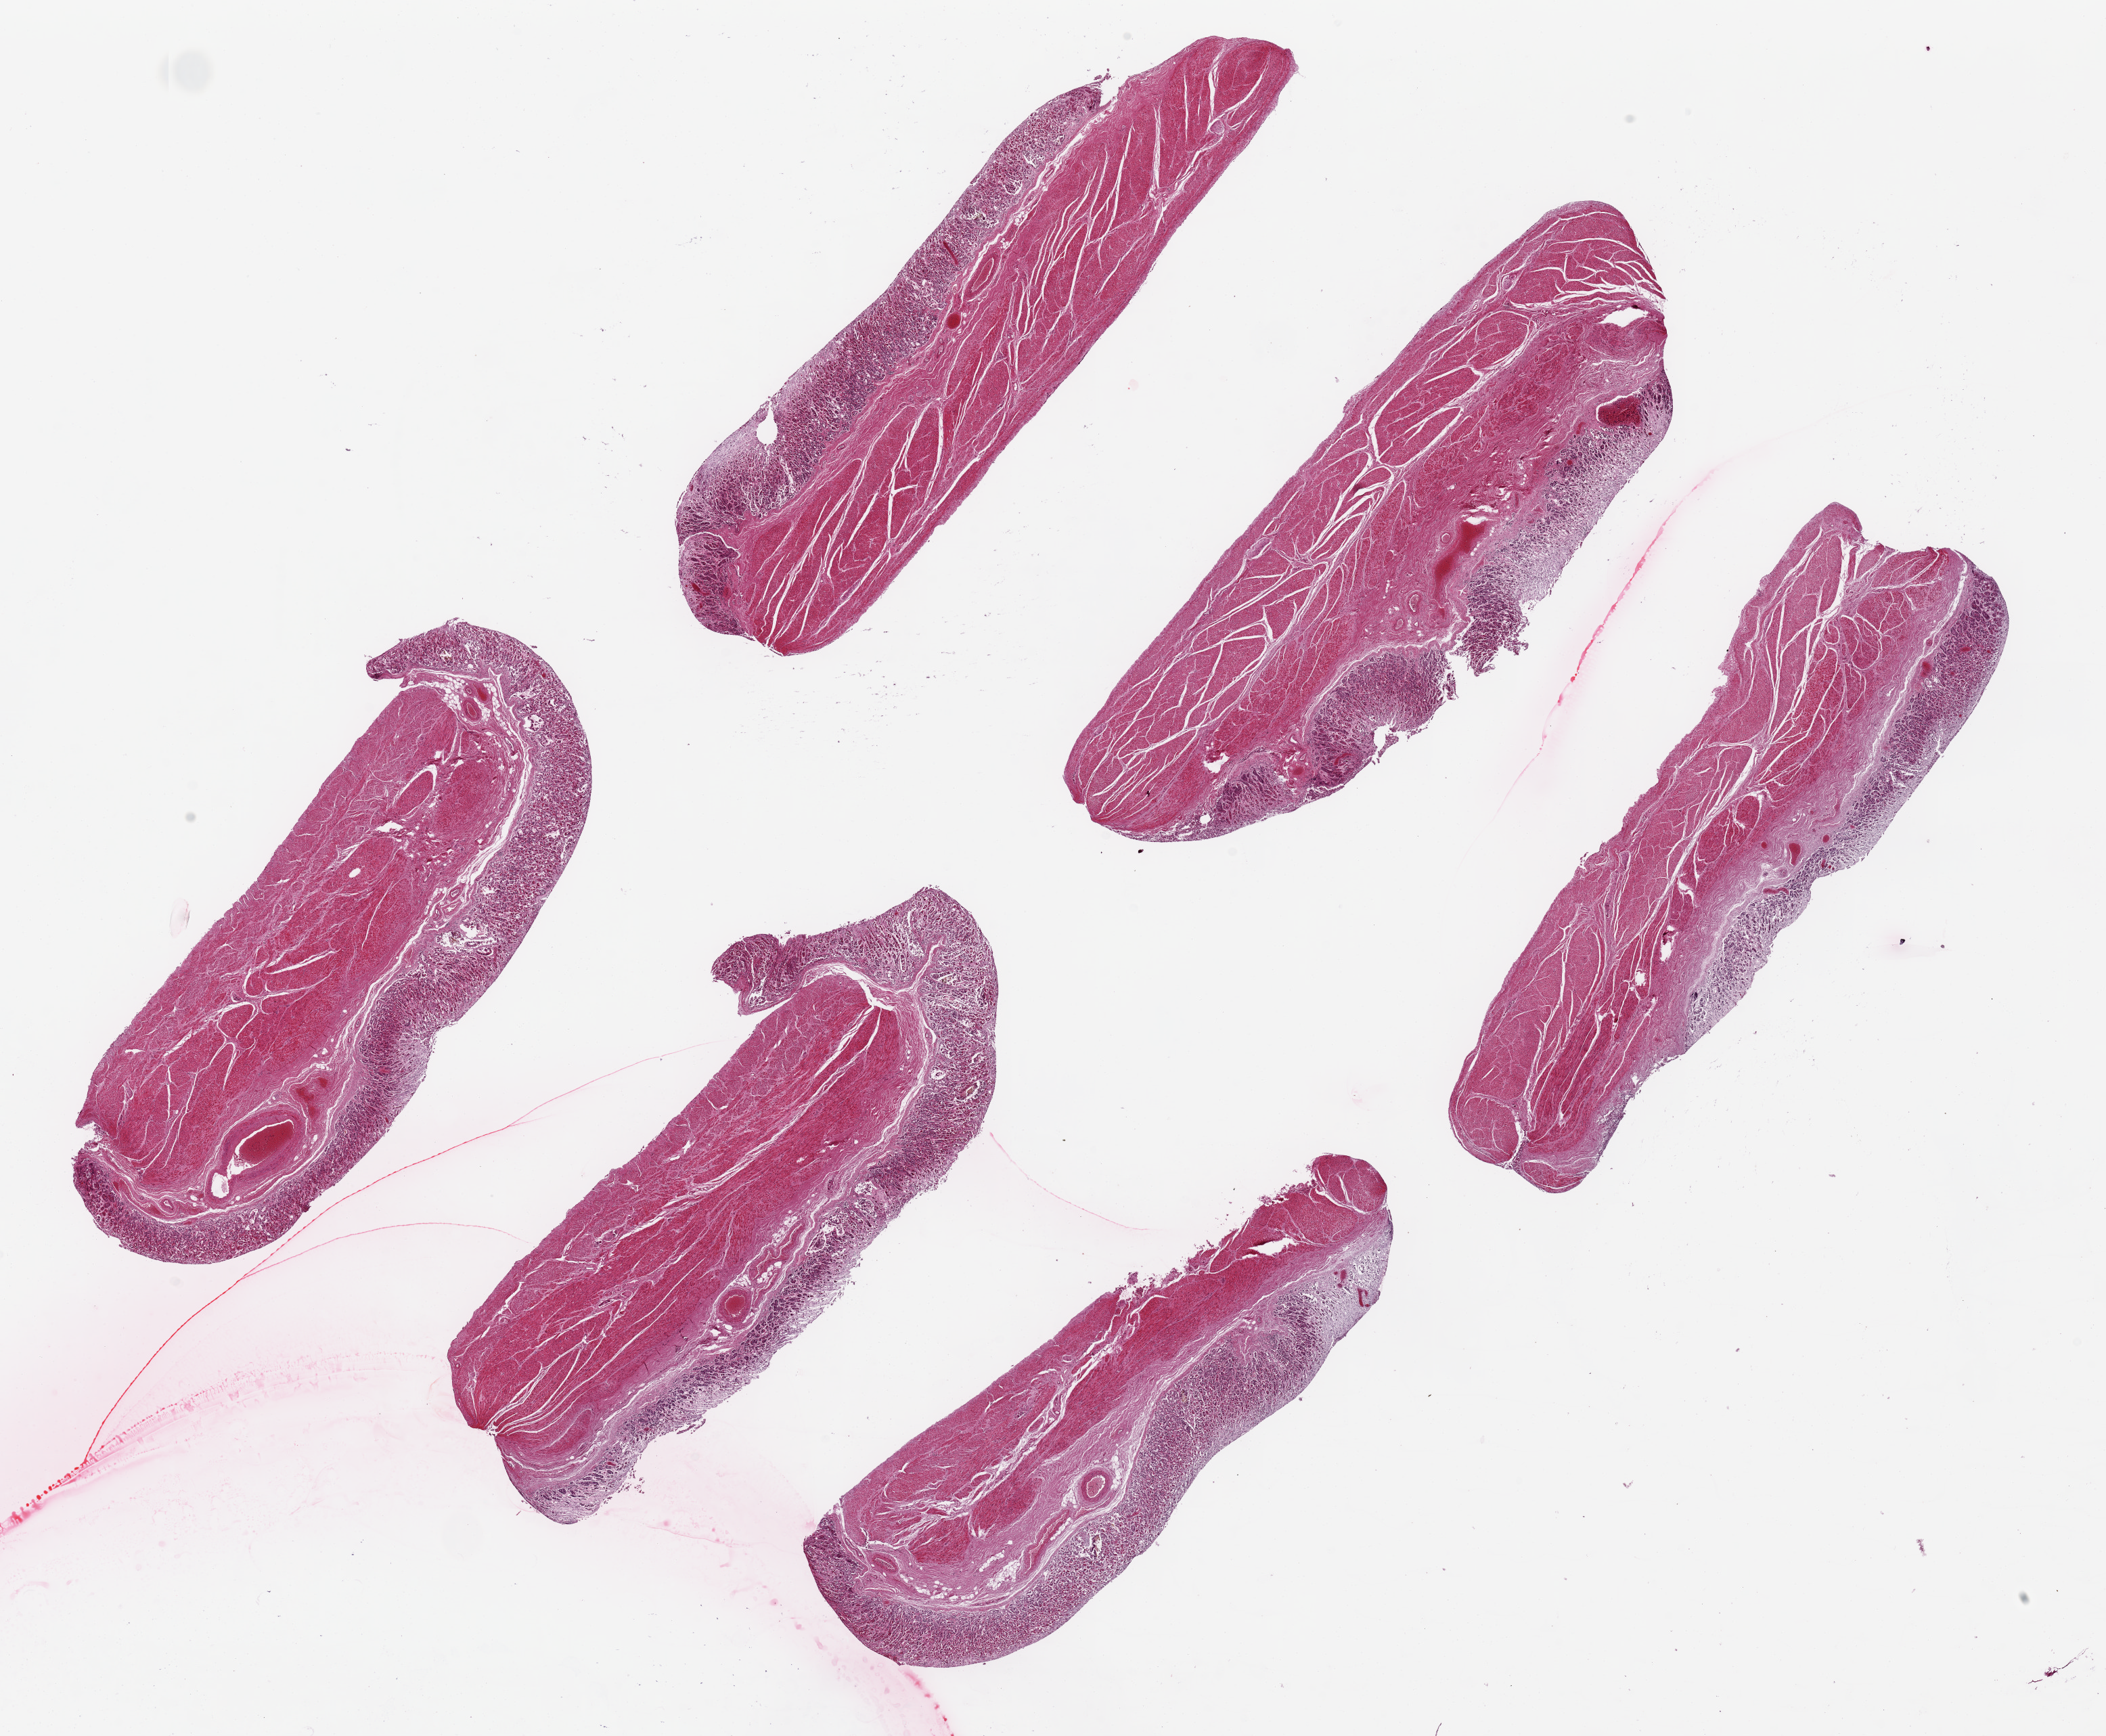
Digitized H&E-stained section, a low-resolution overview of the entire scanned area, about 24.6 x 20.3 mm (from a 20x scan); PAXgene-fixed paraffin-embedded (PFPE) section; section of stomach (target tissue); donor tissue sample. Female donor.
- review note (as recorded): 6 ~8.5x2.5mm pieces, epithelial portions of mucosa with near total autolysis & partly sloughed, 20-30% of thickness